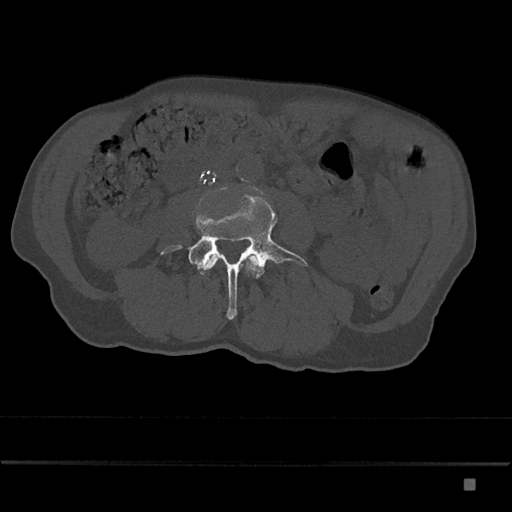
CT including the spine, one axial slice; position 355 of 797 along the scan axis; reconstruction kernel Br40s/3; 120 kVp; bone window (W 1800 / L 400 HU); 0.5 mm slice thickness; 512 × 512 image matrix, field of view 390 × 390 mm. Patient: male, 72 years. Case-level facts recorded for this patient, not image findings: primary cancer: prostate.
Annotated regions visible in this slice (semi-automatic segmentation, software-assisted and operator-edited):
- L3 vertebra: bounding box [x1, y1, x2, y2] px = [204, 255, 258, 270]
- L4 vertebra: [161, 195, 308, 320]